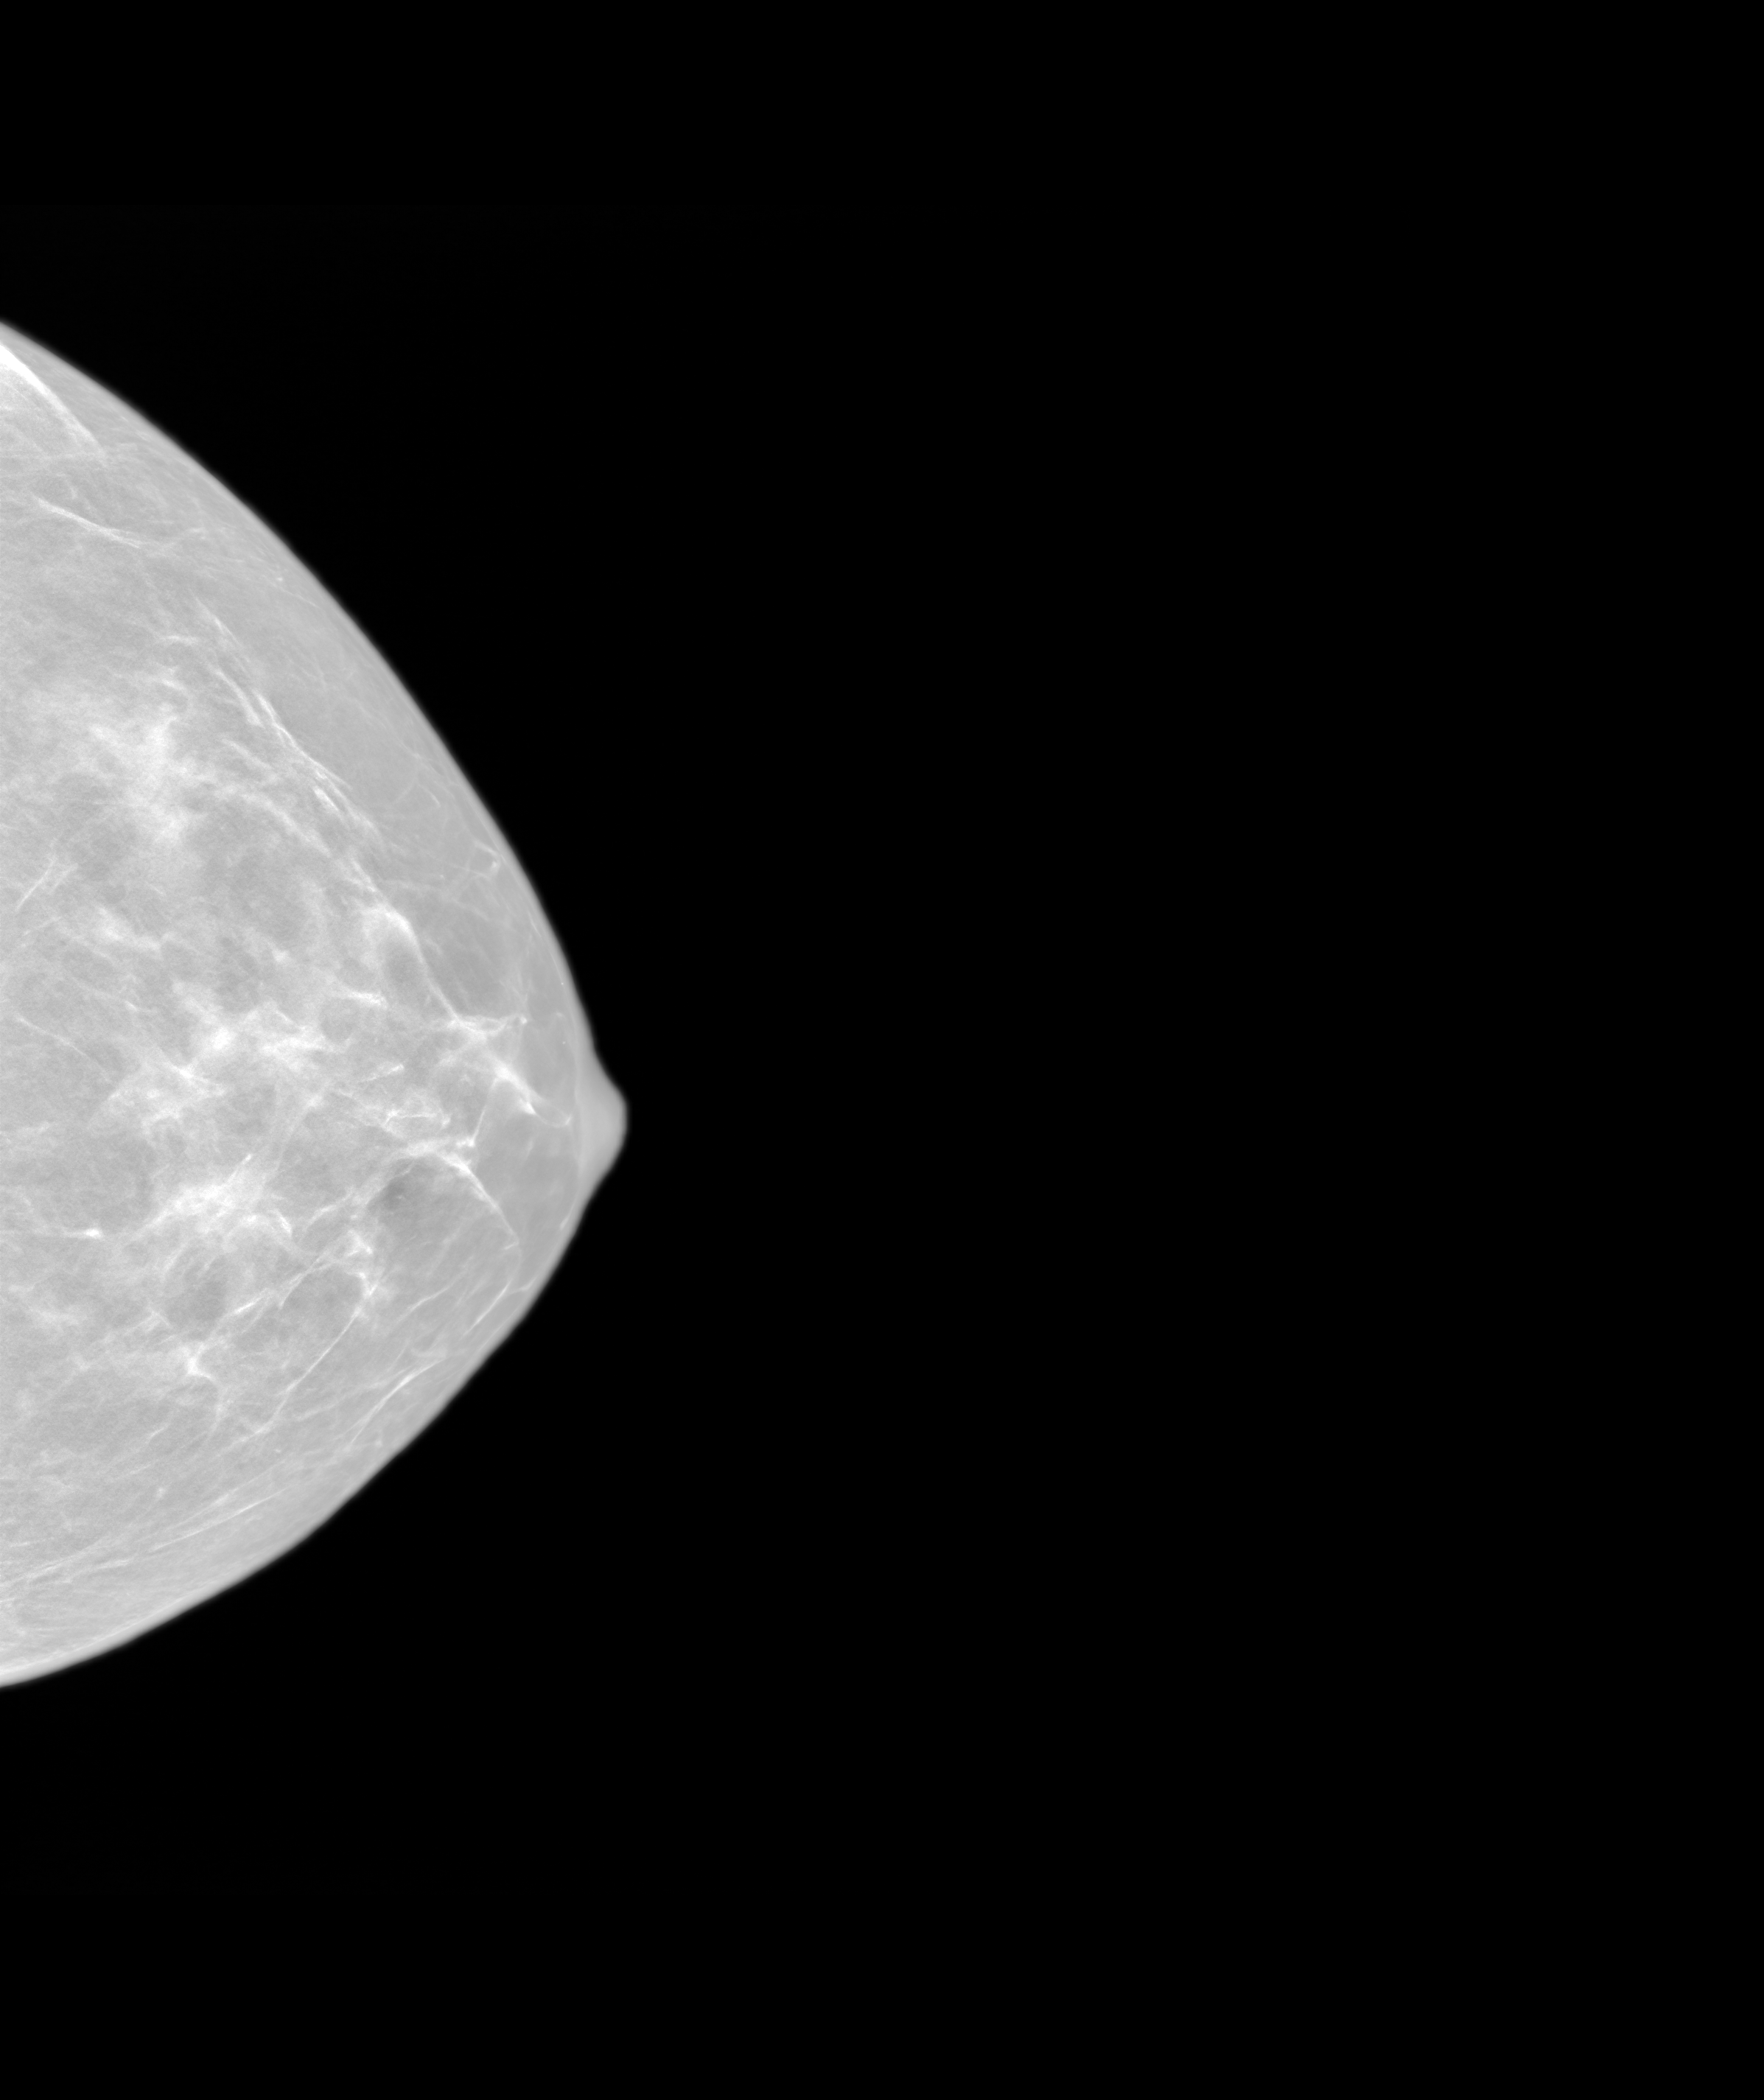
Synthesized 2-D mammogram reconstructed from digital breast tomosynthesis, left breast, craniocaudal (CC) view, screening examination. Patient: female, 43 years.
BI-RADS breast density category at the screening exam (both breasts, scale 1–4): 2. Final BI-RADS assessment for this screening round (tomosynthesis exam, both breasts): category 1. Recall: no recall after this screen.